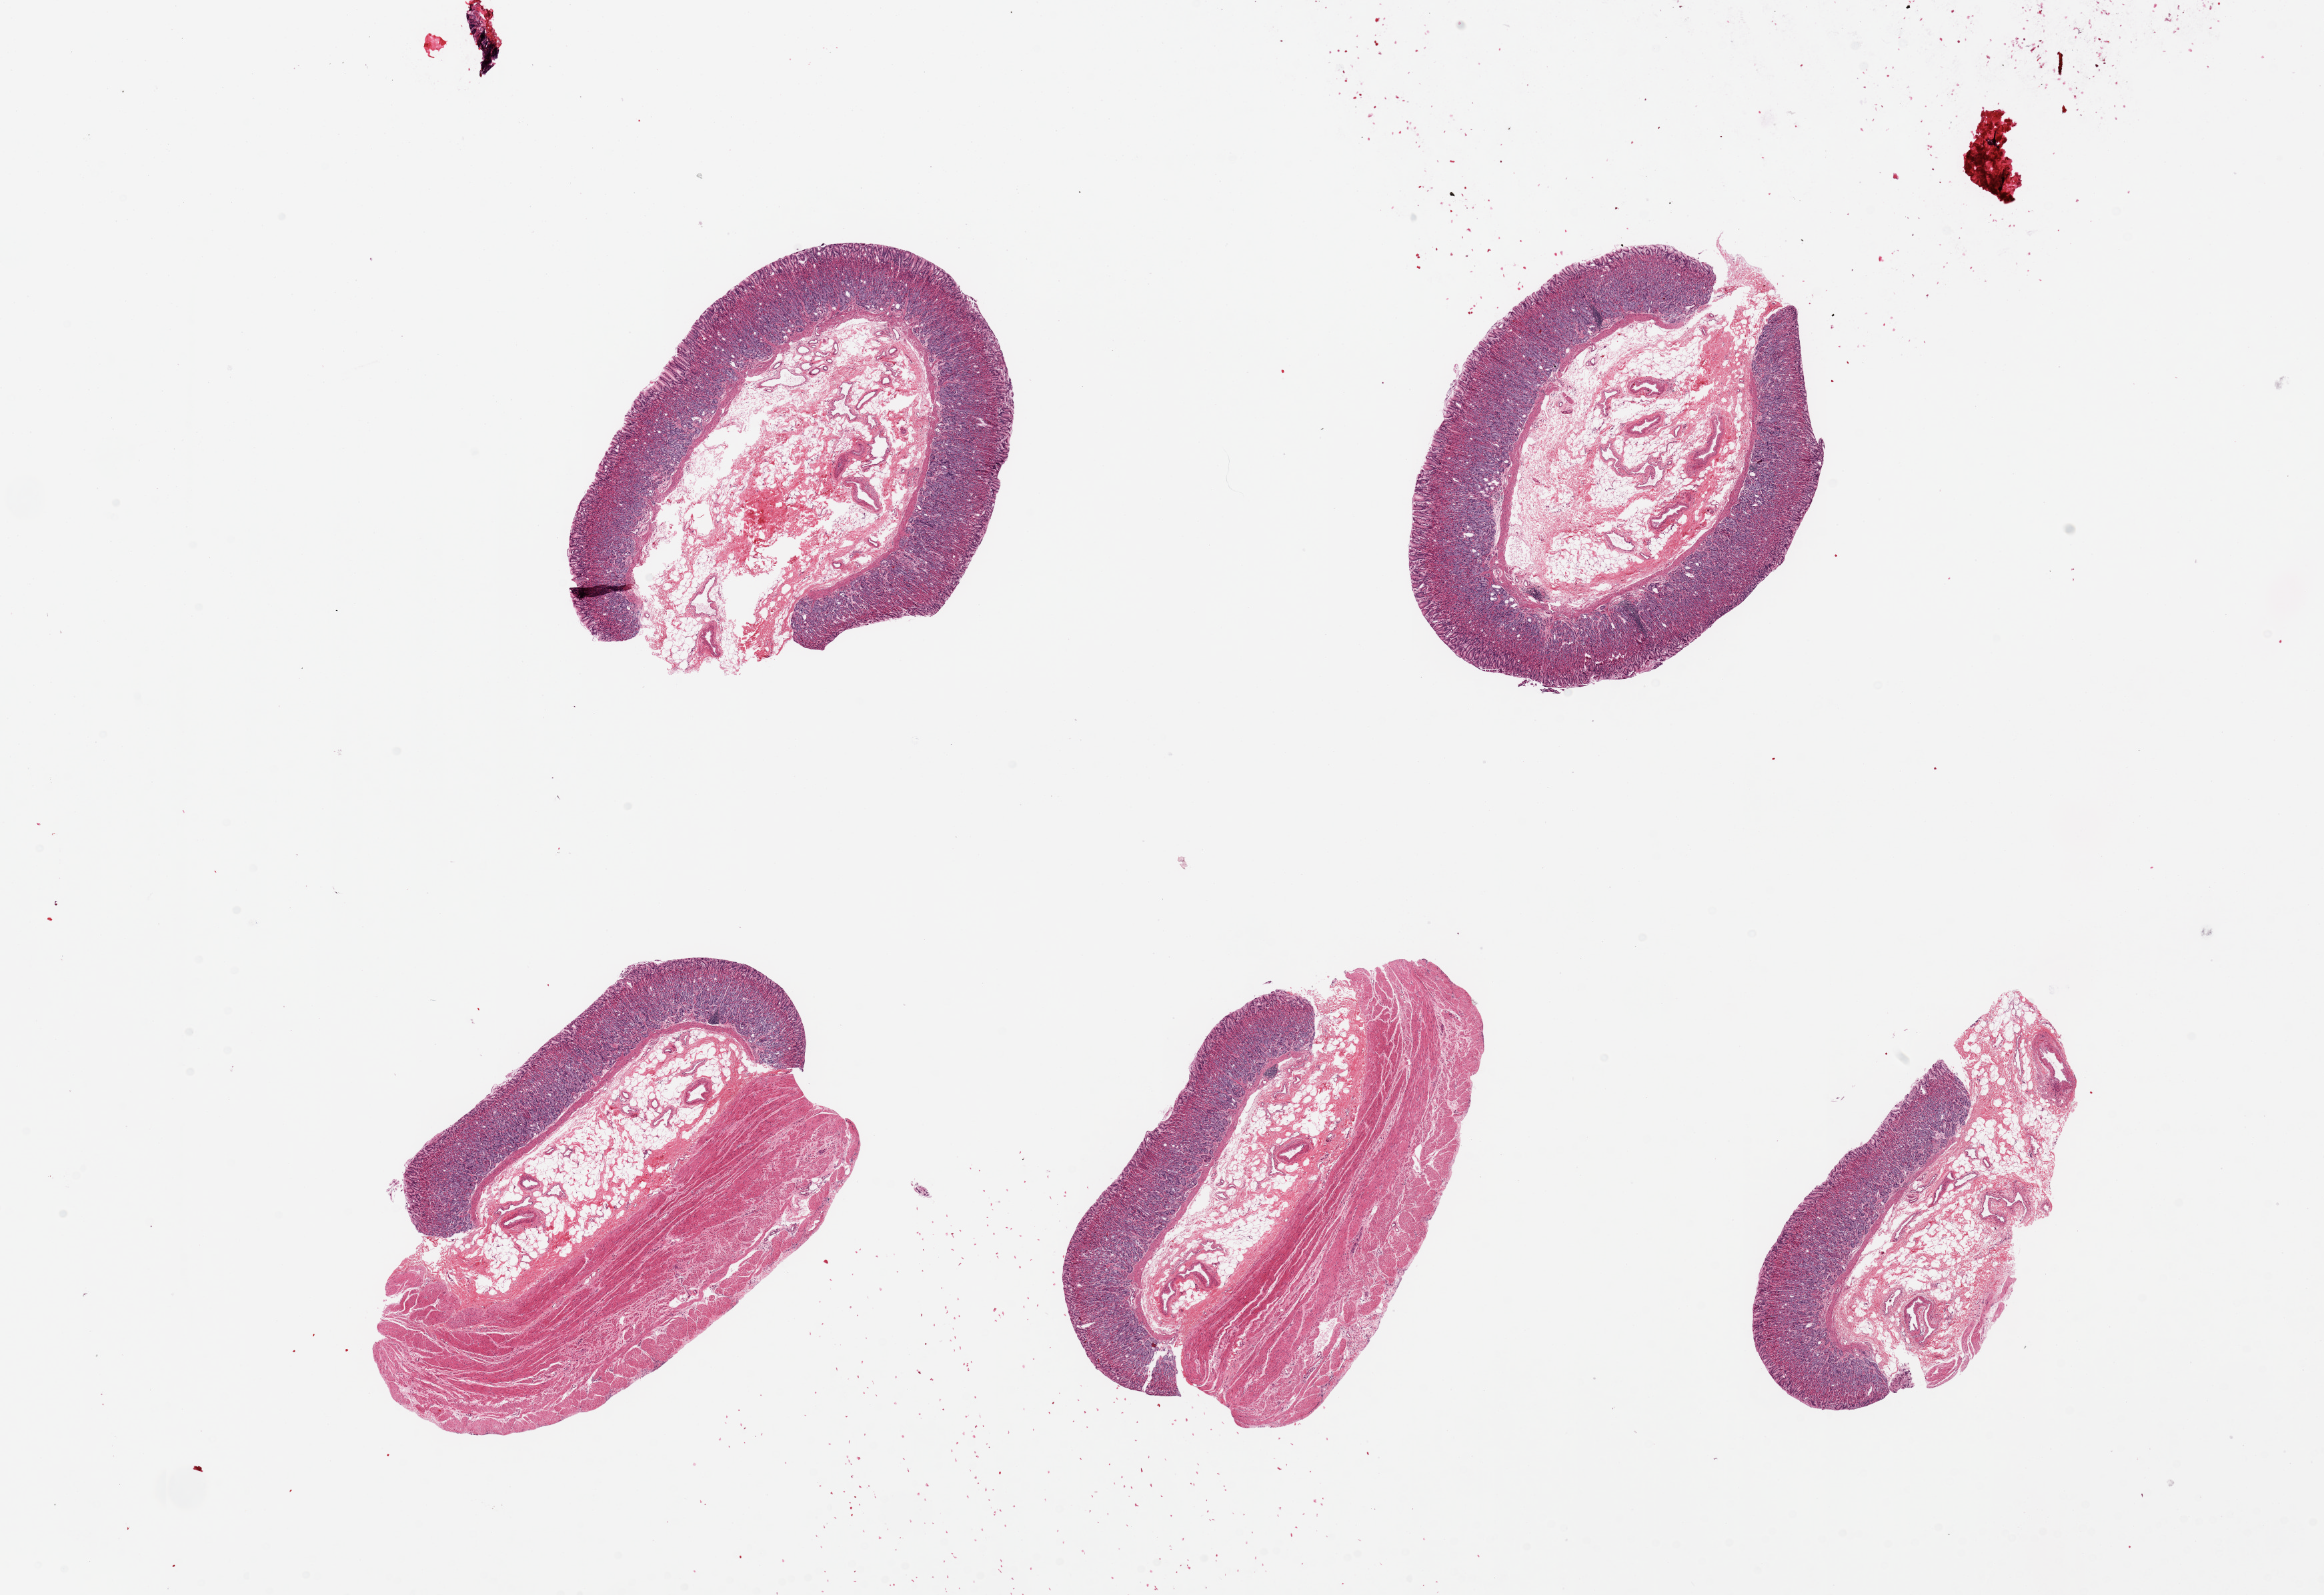
Digitized haematoxylin and eosin-stained section, a low-resolution overview of the entire scanned area, about 27.6 x 18.9 mm (from a 20x scan), PAXgene-fixed, paraffin-embedded tissue, sampled site (target tissue): stomach, donor tissue sample. Male donor.
Pathologist's review note for this sample: 5 pieces: 2 with muscularis propria, 3 without (only have mucosa-submucosa).